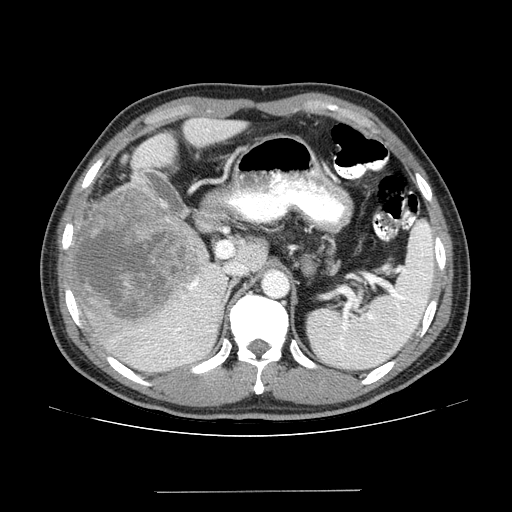
Contrast-enhanced abdominal CT (liver protocol), one axial slice. Position 89 of 131 along the scan axis. 100 kVp. One of 2 acquisitions stored at this slice position. Soft-tissue window (W 400 / L 40 HU). 2.5 mm slice thickness. 512 × 512 image matrix. From the clinical record (not read from this slice): diagnosis: hepatocellular carcinoma (patient treated with transarterial chemoembolisation; whether this scan precedes or follows treatment is not stated here); TNM stage (as recorded): Stage-I; Child-Pugh class: A; tumour differentiation: poorly differentiated; tumour size: 10.3 cm.
Structures marked on this image (semi-automatically segmented with operator editing):
- liver parenchyma outside the tumour (the mass and vessels are separate outlines, so this box may not span the whole liver): bounding box <64,118,246,372> (left, top, right, bottom; pixels)
- mass: <67,187,208,327>
- liver vessels: <146,129,214,361>